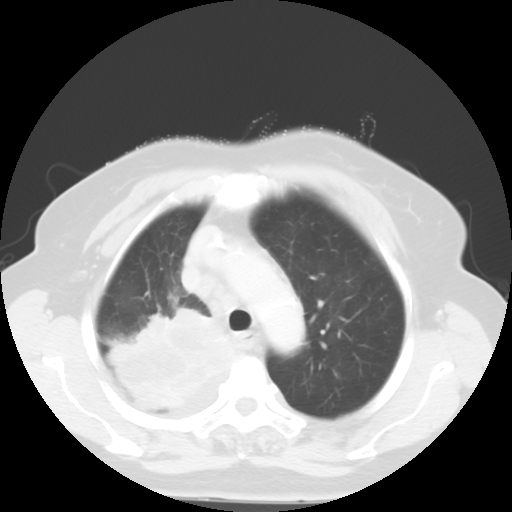
Chest CT, one axial slice. Slice 41 of 52 in the series (ordered by position). Lung window (W 1500 / L -600 HU). 512 × 512 image matrix, field of view 333 × 333 mm. Female patient, age 81 years. From the clinical record (not read from this slice): clinical TNM (as recorded): T4 N3 M1b.
Structures marked on this image (bounding box drawn by a radiologist):
- lung tumour (recorded histology: adenocarcinoma): box from (x=107, y=300) to (x=236, y=415) px